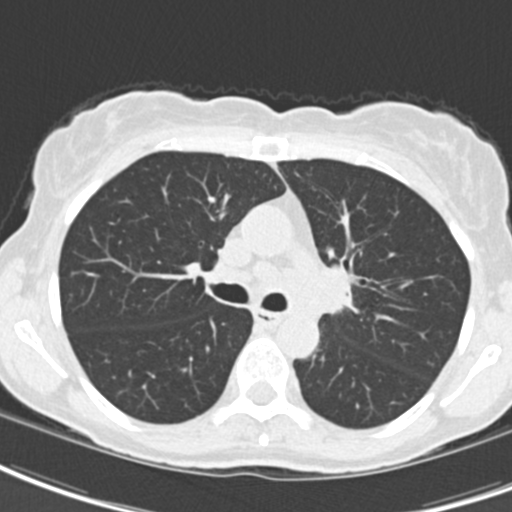
Chest CT (low-dose screening protocol), one axial image; baseline screening round; lung window (W 1500 / L -600 HU); 2 mm slice thickness; standard (soft-tissue) reconstruction kernel (B30f); slice 62 of 189 in the series. Female participant, aged 62 years at enrolment.
• Expert-annotated lung lesion, box from (x=294, y=249) to (x=369, y=333) px.
• Reader record for this screening exam (exam-level; its link to the box is not recorded): non-calcified nodule or mass ≥4 mm, right upper lobe, 24 × 20 mm, smooth margins, ground glass attenuation.
• Note: the box lies in the patient's left hemithorax on this image, whereas the reader's record names the right lung; they may be different findings.
• Official screen result: positive, change unspecified: nodule(s) >= 4 mm or enlarging nodule(s), mass(es), or other non-specific abnormalities suspicious for lung cancer.
• Later outcome: lung cancer diagnosed 24 days after this screen — oat cell carcinoma, left hilum, left main stem bronchus, stage IIIB (AJCC 6th edition), 50 mm at pathology.